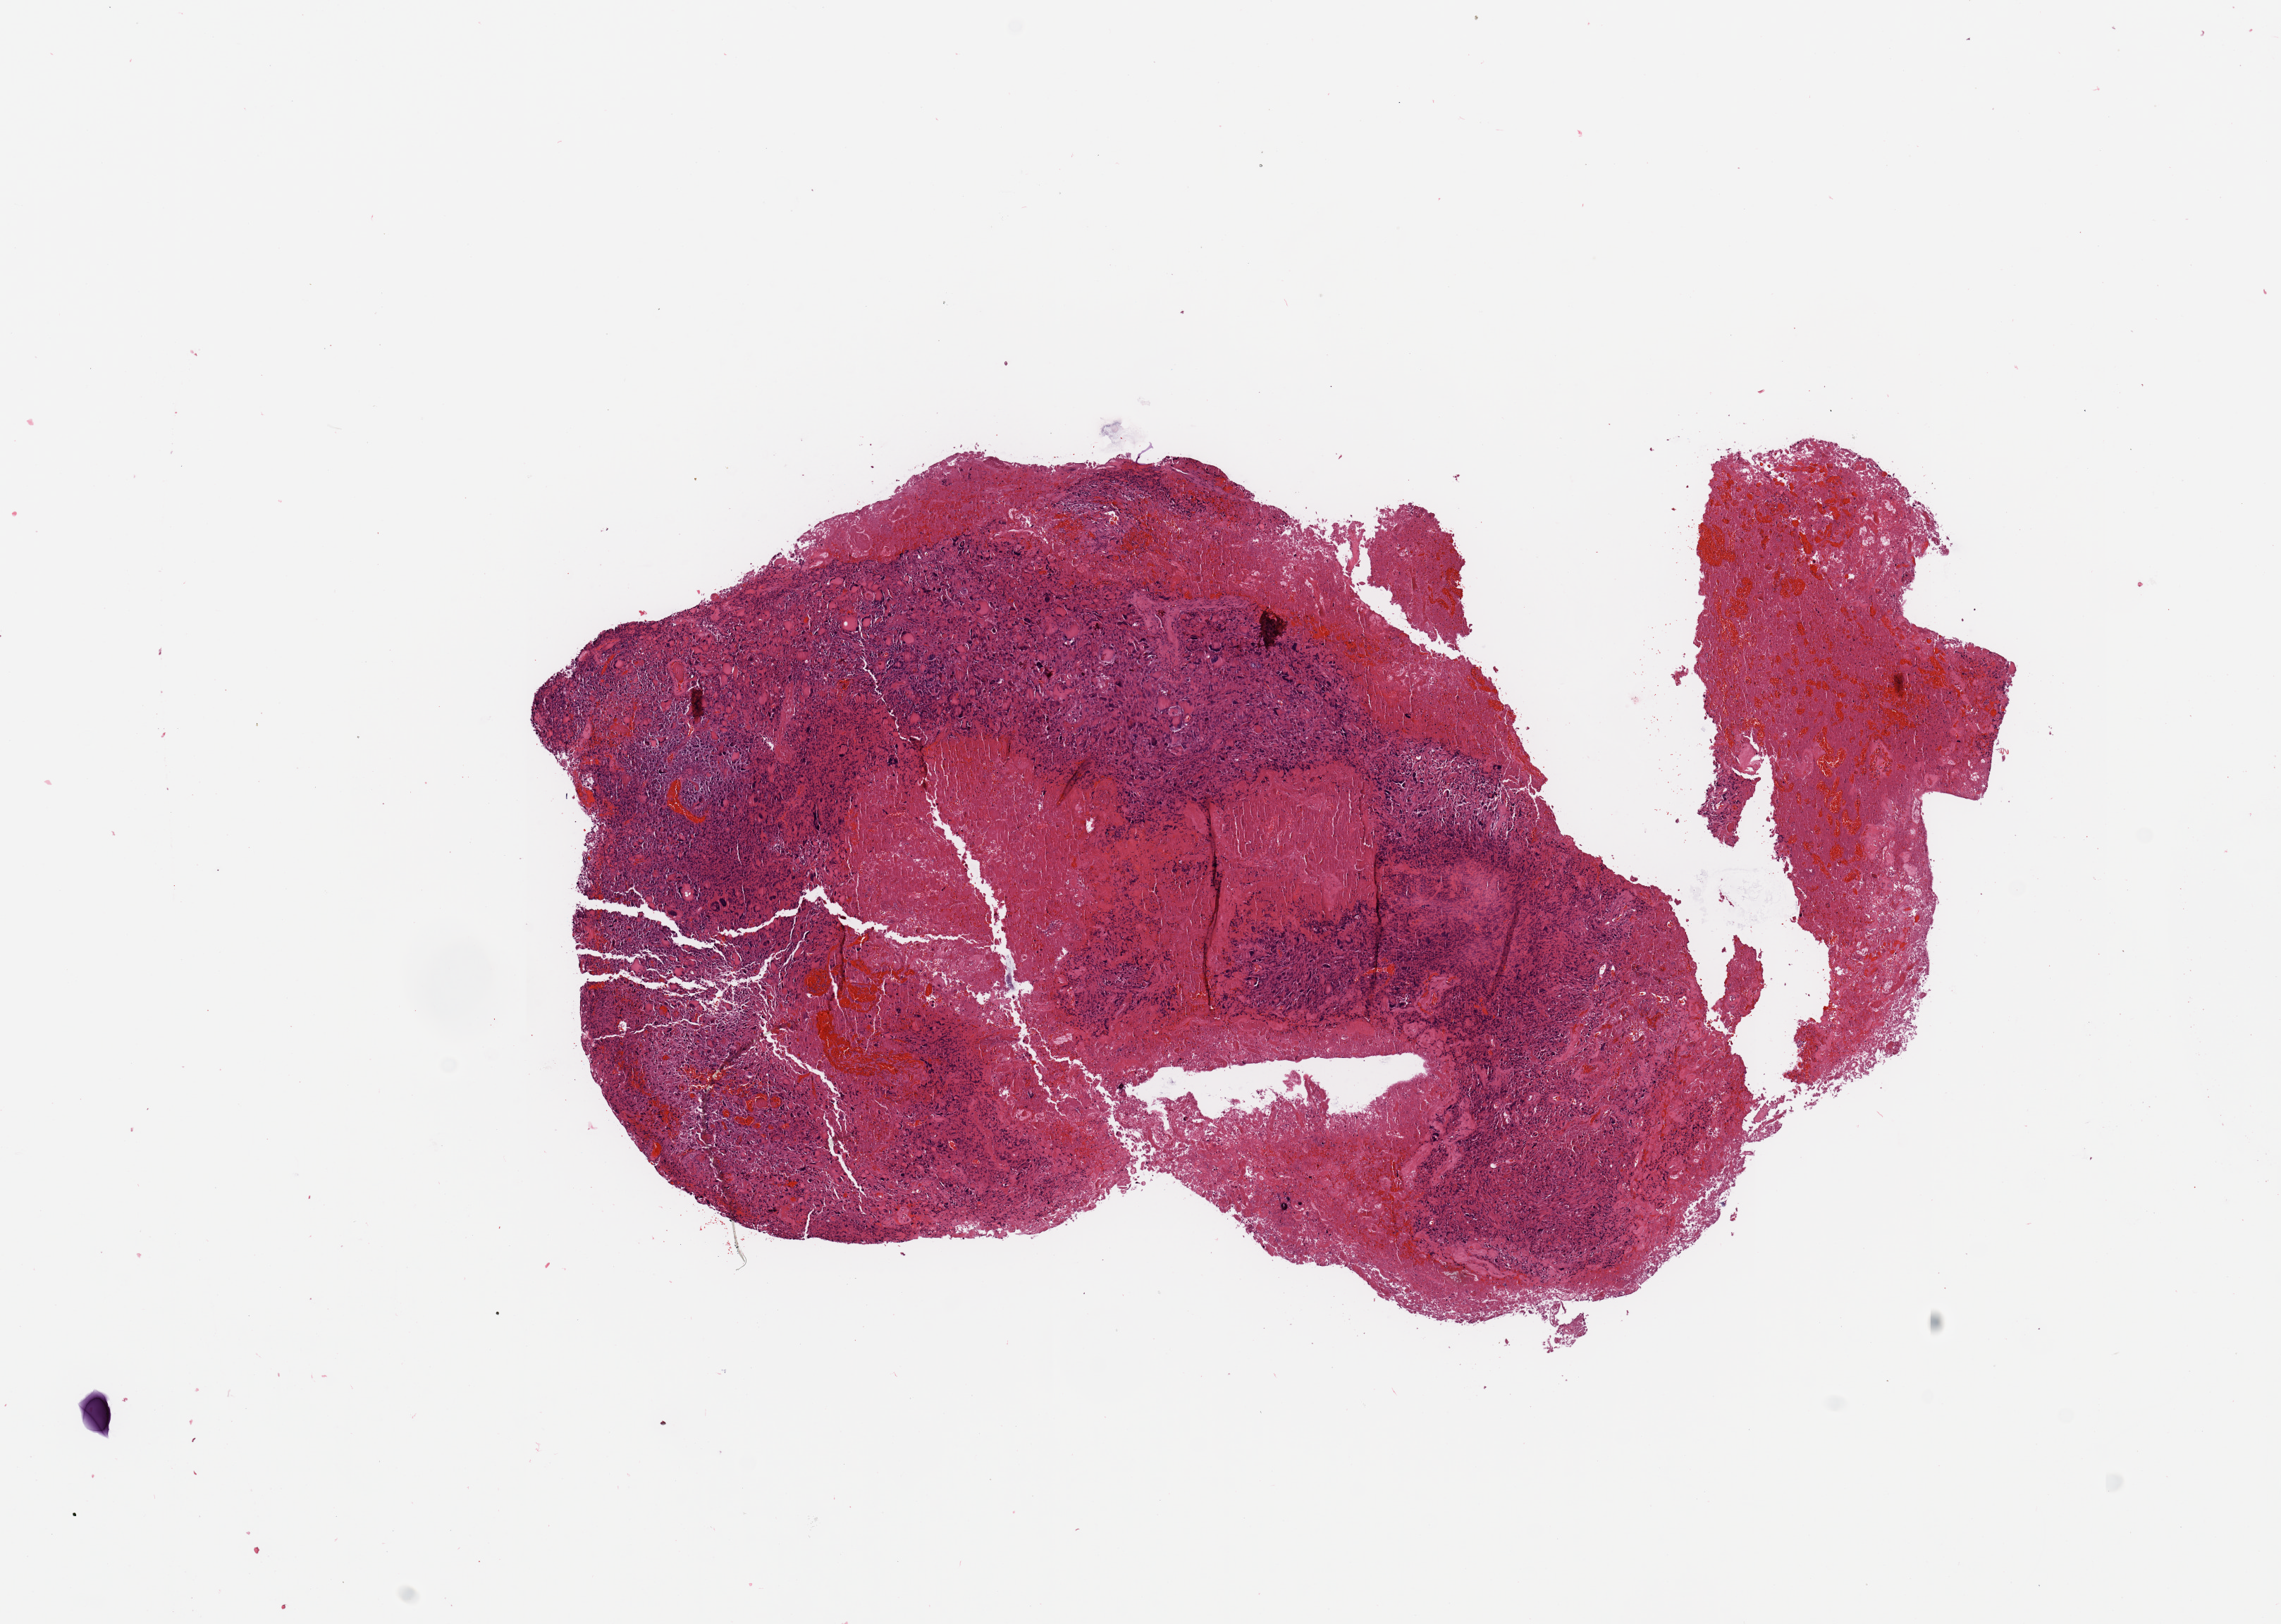
Hematoxylin and eosin (H&E) stained whole-slide image, whole scanned area (about 12.8 x 9.1 mm, slide scanned at 20x) shown as a low-resolution overview. Brain, tumour tissue. 69-year-old female patient.
Primary tumour site (as recorded): frontal lobe. Diagnosis: Glioblastoma.